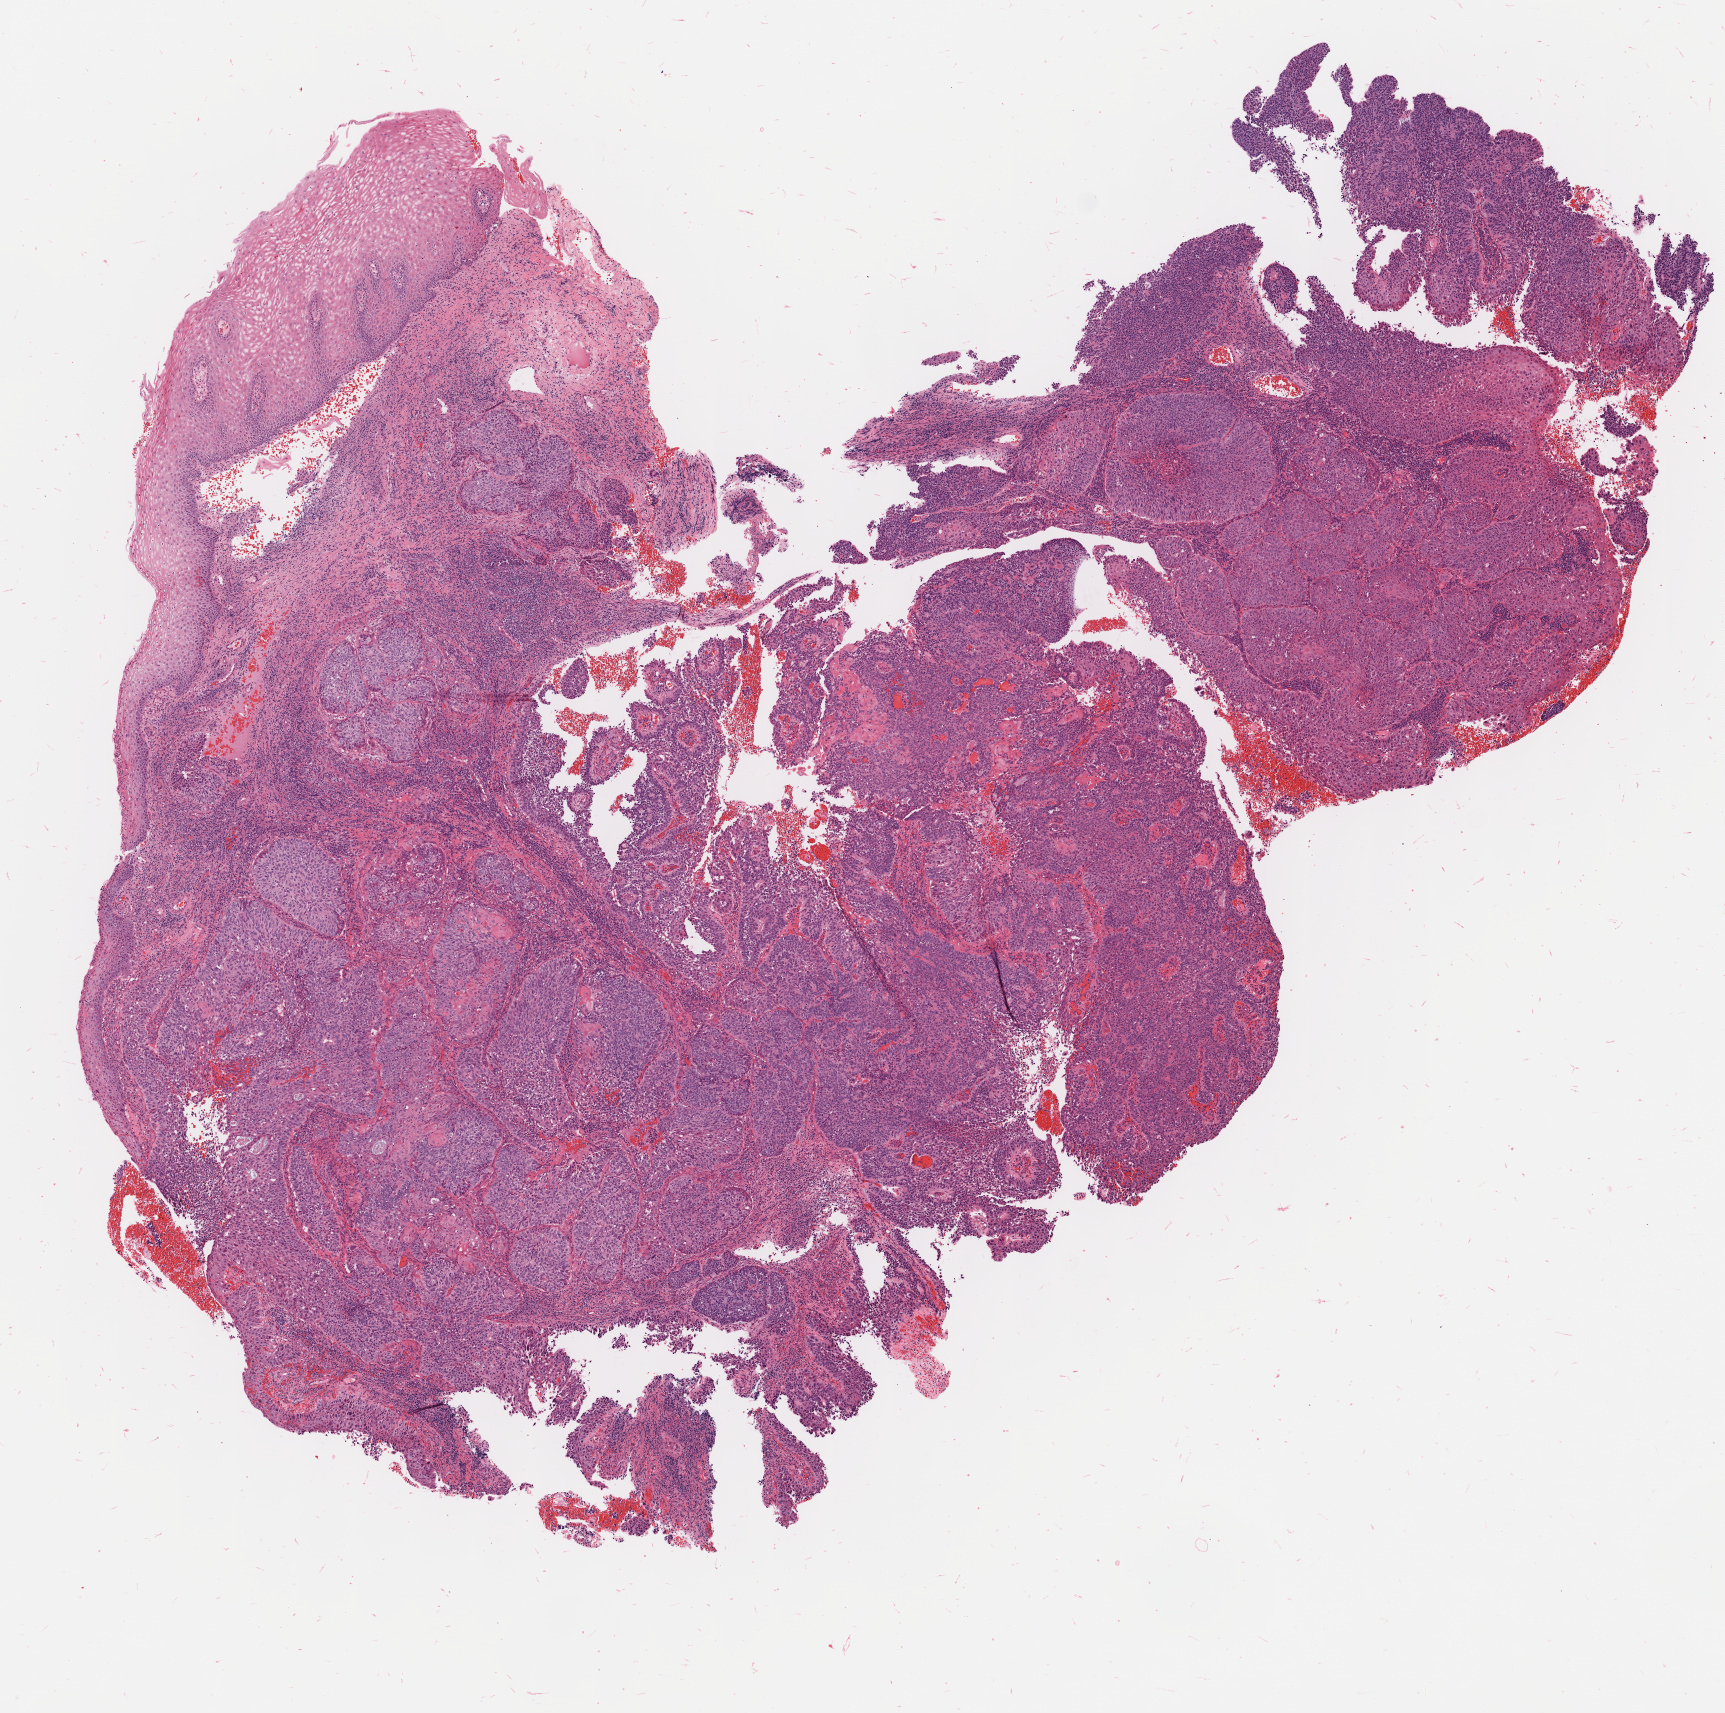
H&E whole-slide image — whole scanned area (about 6.9 x 6.8 mm) shown as a low-resolution overview; tumor tissue; anatomic site: cervix. Patient: female, 63 years old.
Histologic diagnosis: Squamous cell carcinoma, large cell, nonkeratinizing, NOS.